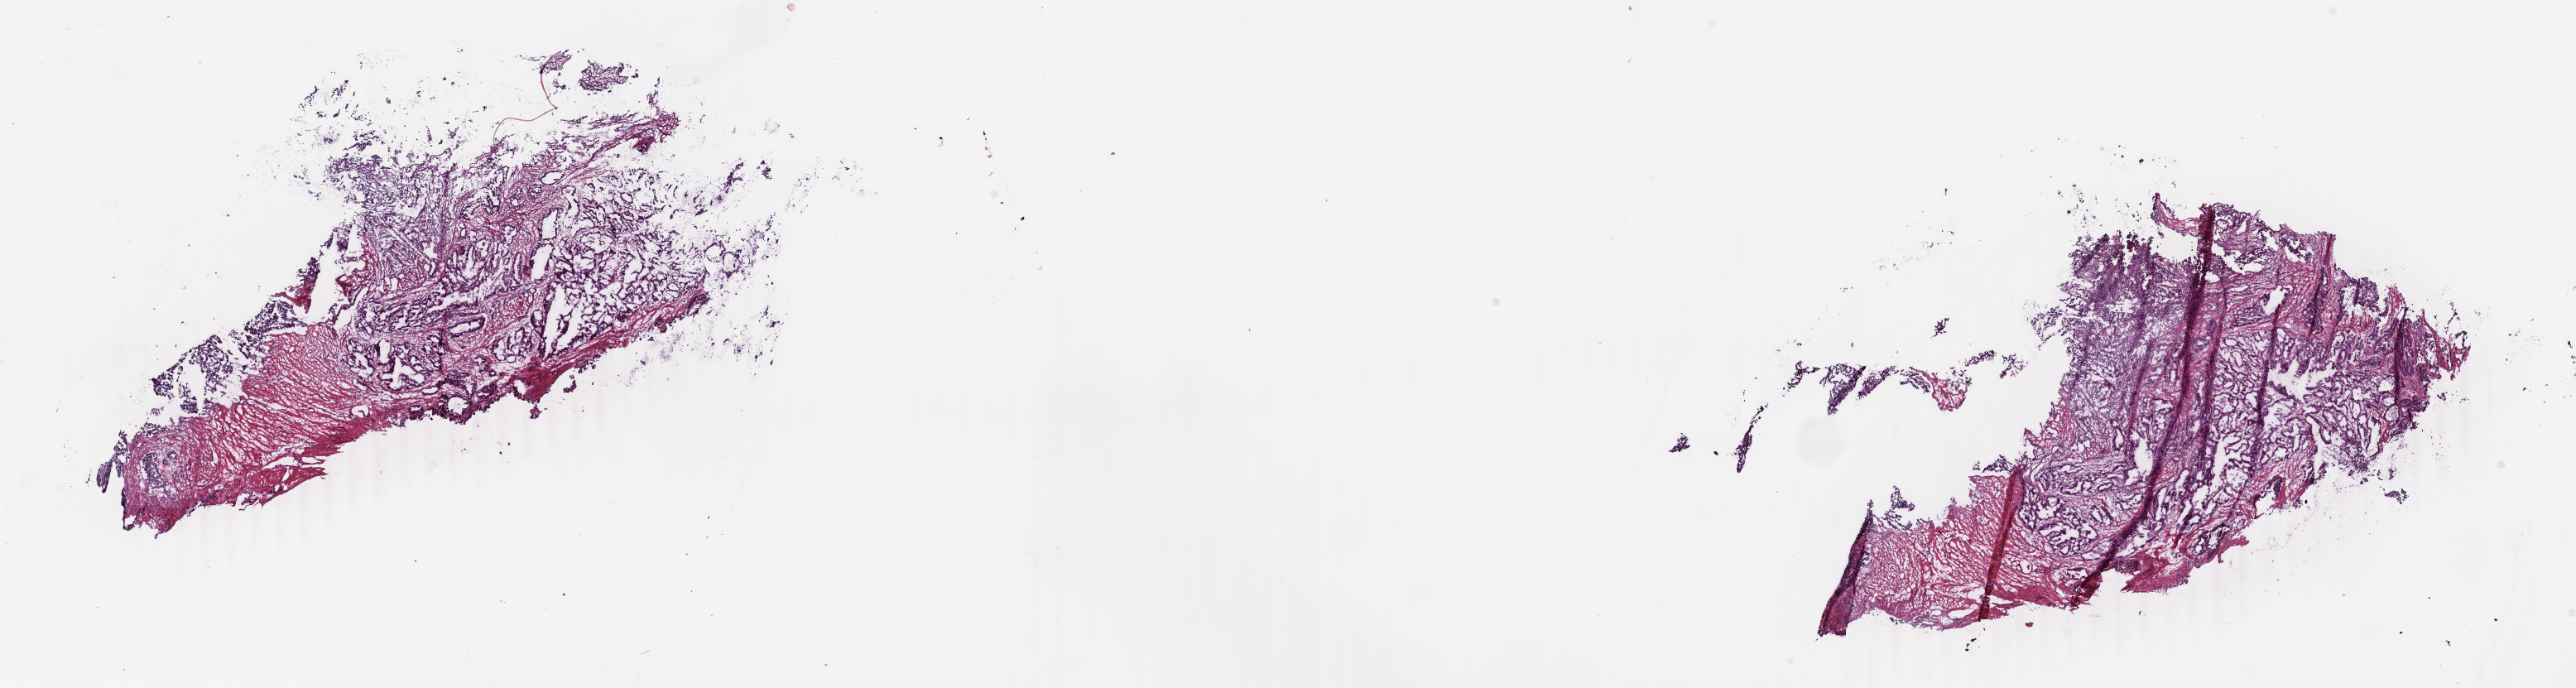
H&E whole-slide image, a low-resolution overview of the entire scanned area, about 24.7 x 6.6 mm, frozen section from the bottom of the tissue portion, uterus, primary tumour sample. Female, age 68 years at initial diagnosis. Histologic grade: G3 (poorly differentiated). Composition of this section per pathologist review: tumour cells 40%, tumour nuclei 45%, normal cells 0%, stromal cells 50%, necrosis 10%. Inflammatory infiltration, as recorded: lymphocyte infiltration 10%, monocyte infiltration 20%, neutrophil infiltration 20%.
• FIGO stage: IB
• histologic diagnosis: Endometrioid adenocarcinoma, NOS (endometrium)